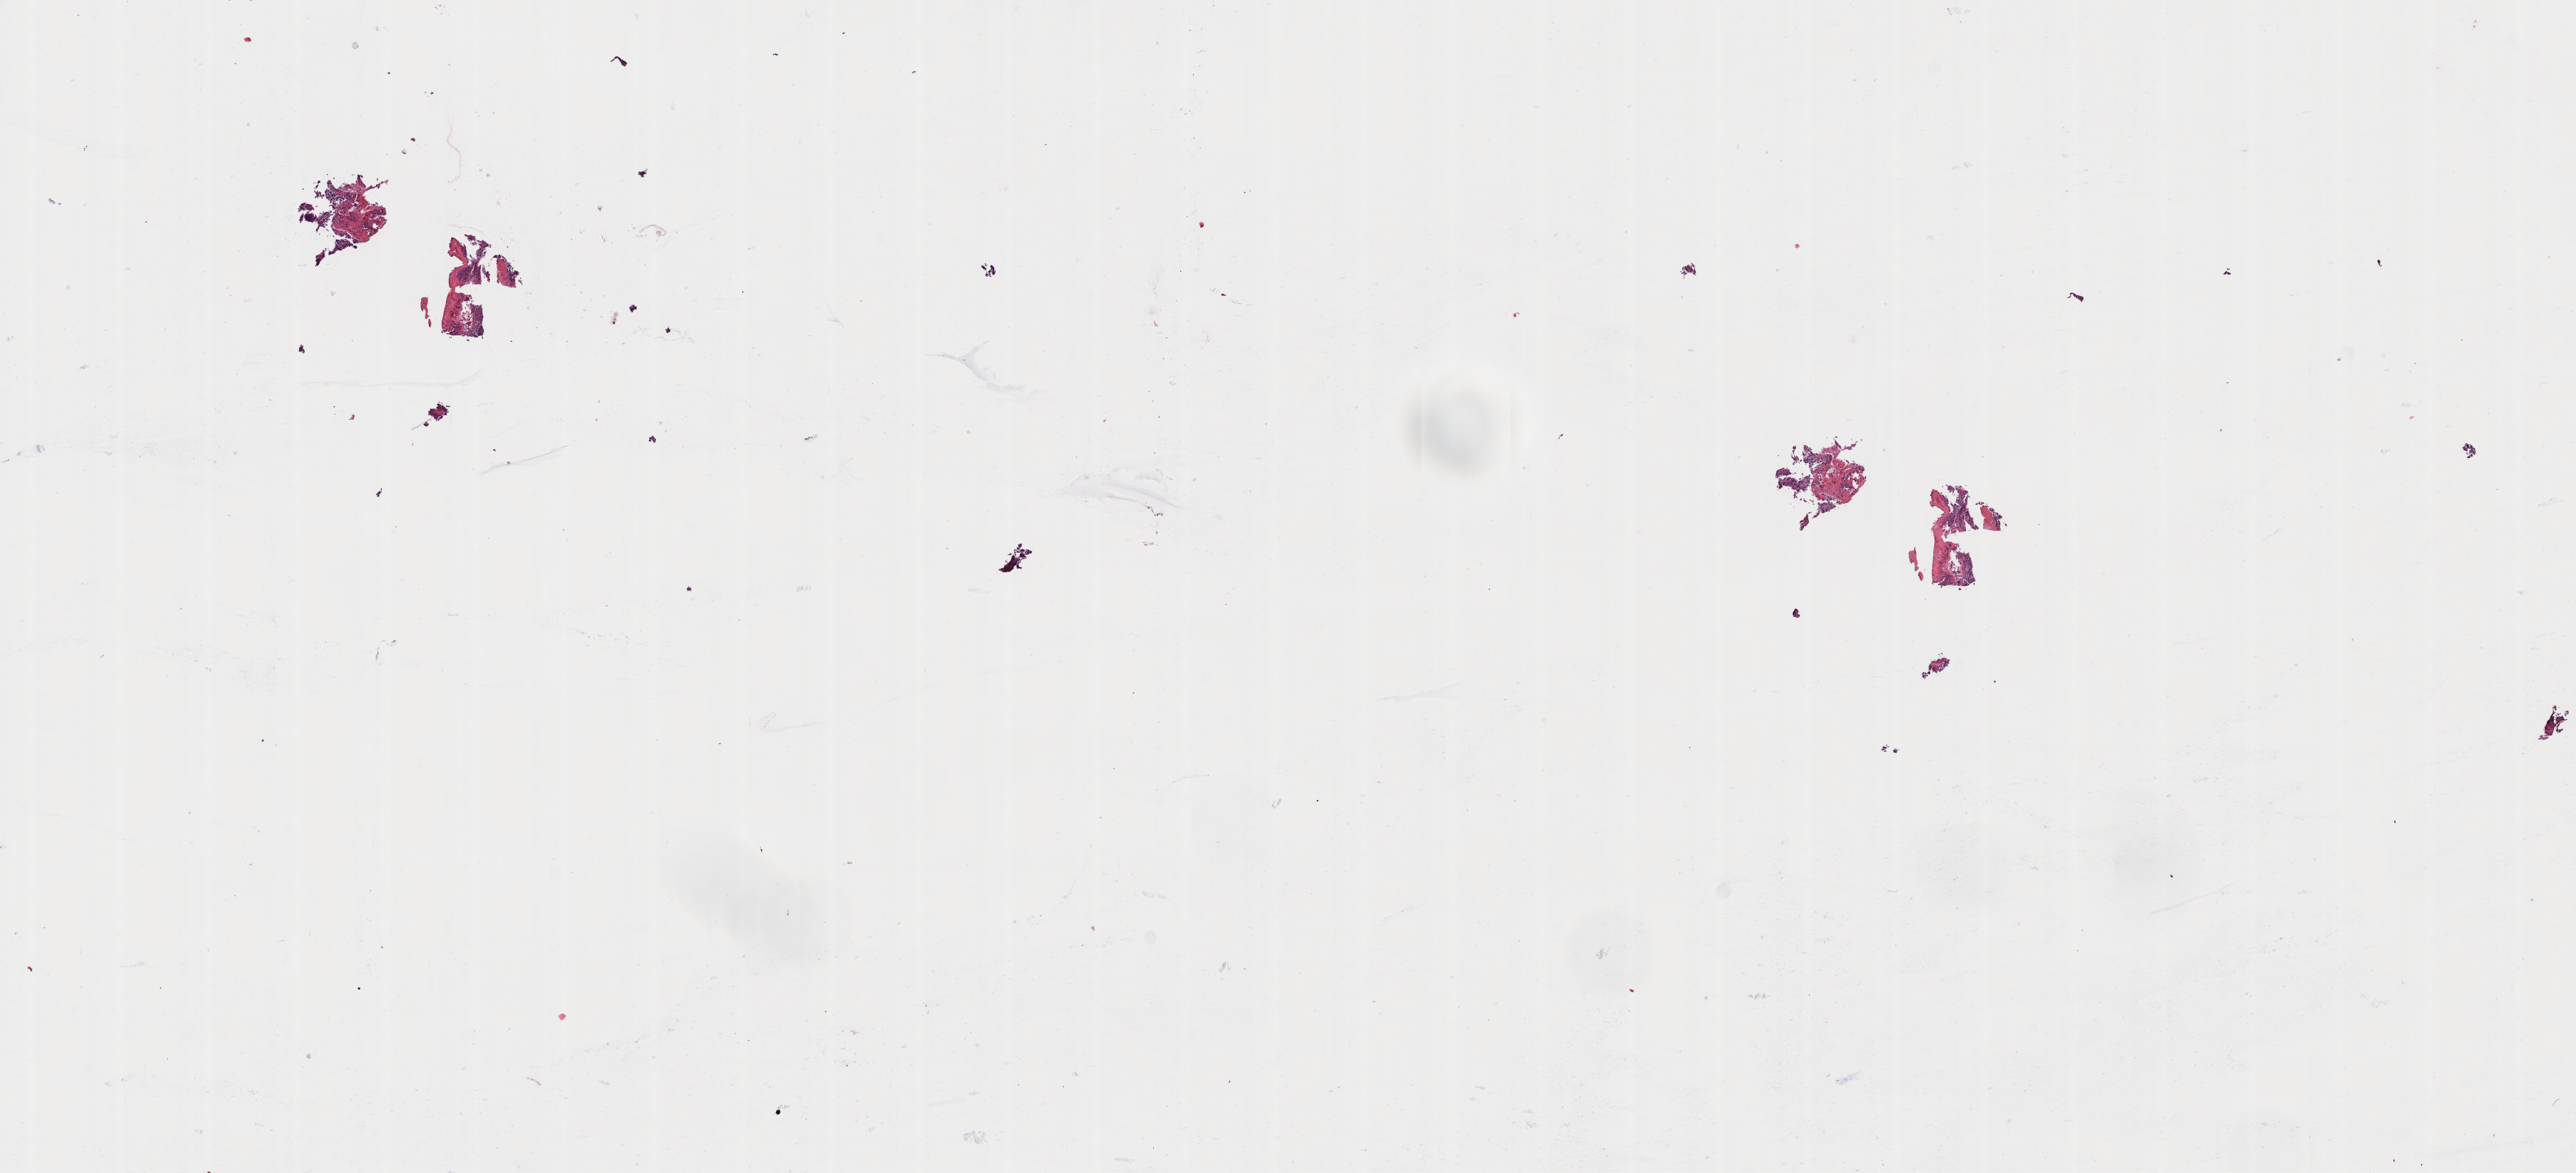
Digitized H&E-stained tissue section (whole slide) — whole scanned area (about 14.6 x 6.6 mm) shown as a low-resolution overview; FFPE section; primary tumour sample from the skin. Female, age 66 years at initial diagnosis.
Histologic diagnosis: Malignant melanoma, NOS.